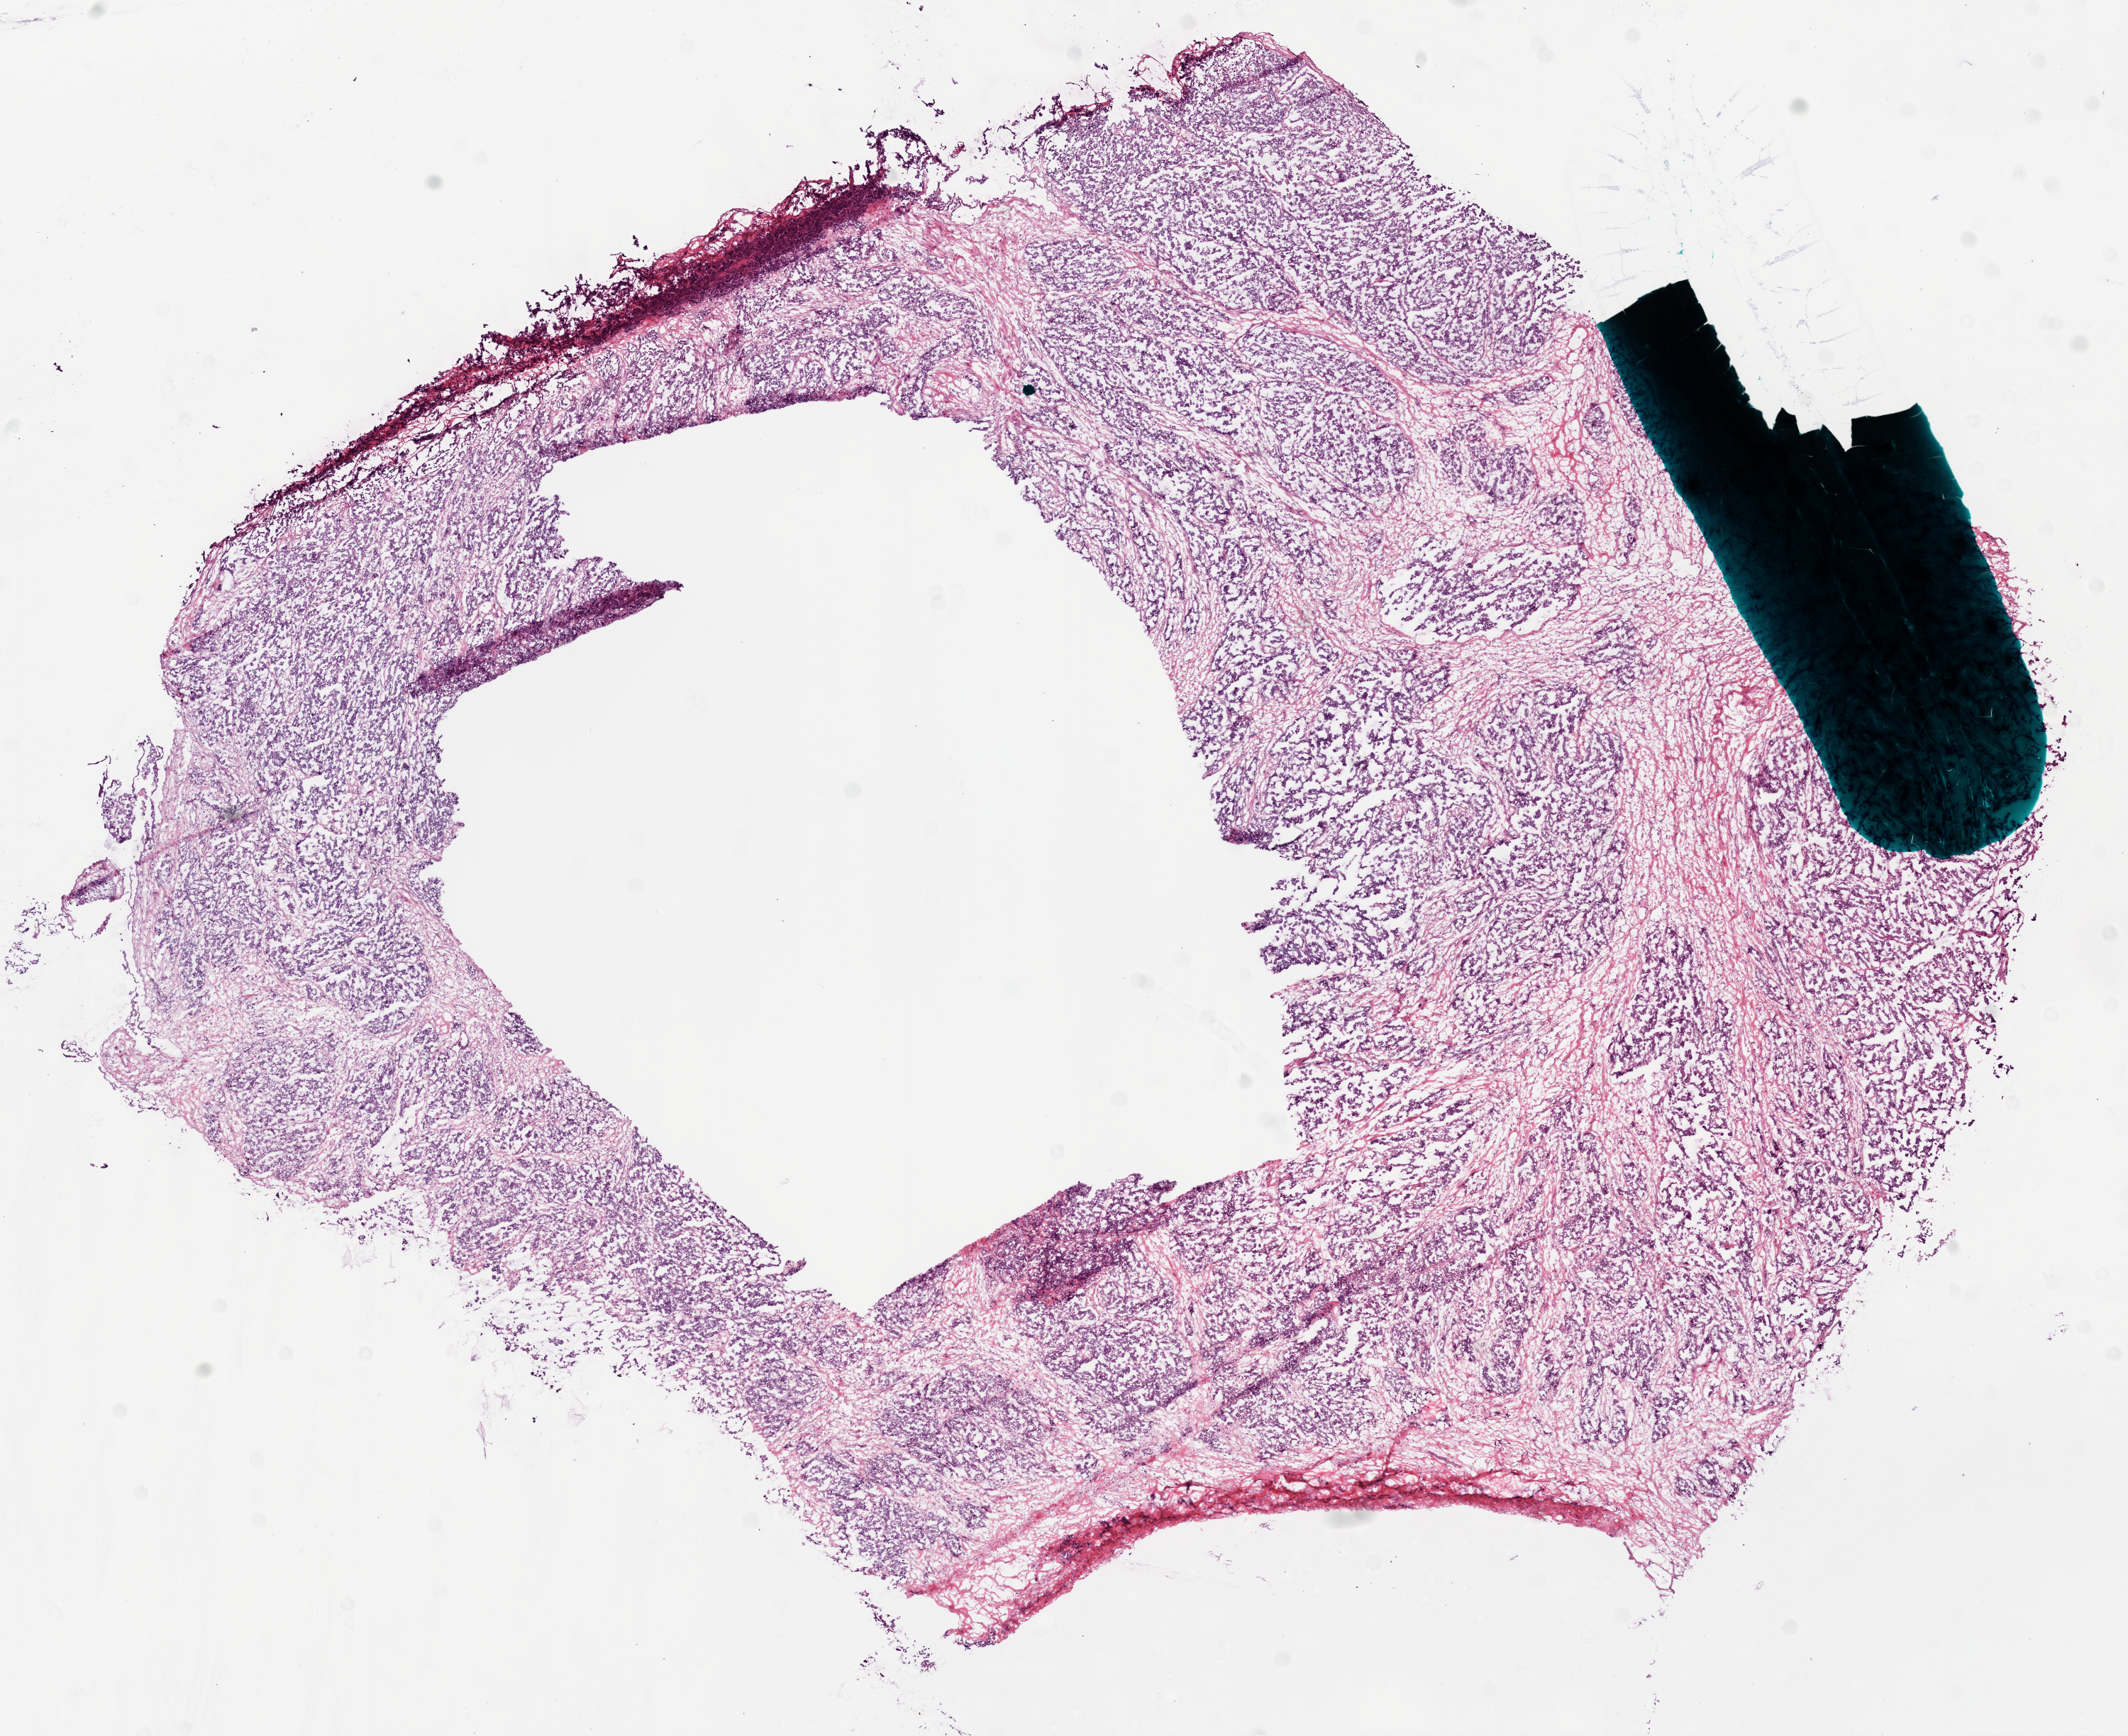
Whole-slide histology image, H&E, shown as a low-resolution overview of the whole scanned area (about 12.0 x 9.8 mm, slide scanned at 20x), frozen section, primary tumour sample from the ovary. Patient: female, age at initial diagnosis 48 years. Histologic grade: G3 (poorly differentiated). Pathologist review of this section (percent, as recorded): tumour cells 89%, tumour nuclei 90%, normal cells 0%, stromal cells 10%, necrosis 1%.
Pathologic diagnosis: Serous cystadenocarcinoma, NOS. FIGO stage: IIIC. Laterality: bilateral.